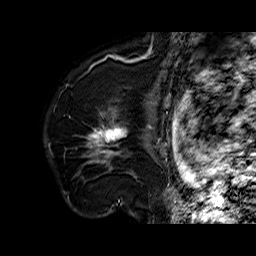
Breast MRI (dynamic contrast-enhanced), one sagittal slice. Slice 46 of 60 in the series (ordered by position). Dynamic contrast-enhanced series, time point 2 of 6 at this slice position (early post-contrast). 1.5 T. TE 6.4 ms, TR 32.7 ms. 4 mm slice thickness. 256 × 256 image matrix, field of view 200 × 200 mm. Female patient. From the clinical record (not read from this slice): setting: breast cancer imaged before/during neoadjuvant chemotherapy; receptor status: HR-positive, HER2-negative.
Outlined on this slice (semi-automatically segmented with operator editing):
- analysis volume of interest (the breast-tissue region the enhancement analysis was run in; not a lesion): bounding box [x1, y1, x2, y2] px = [74, 110, 138, 179]
- tumour enhancement mask (voxels above the 100 % enhancement threshold inside the analysis volume of interest): [89, 124, 126, 163]